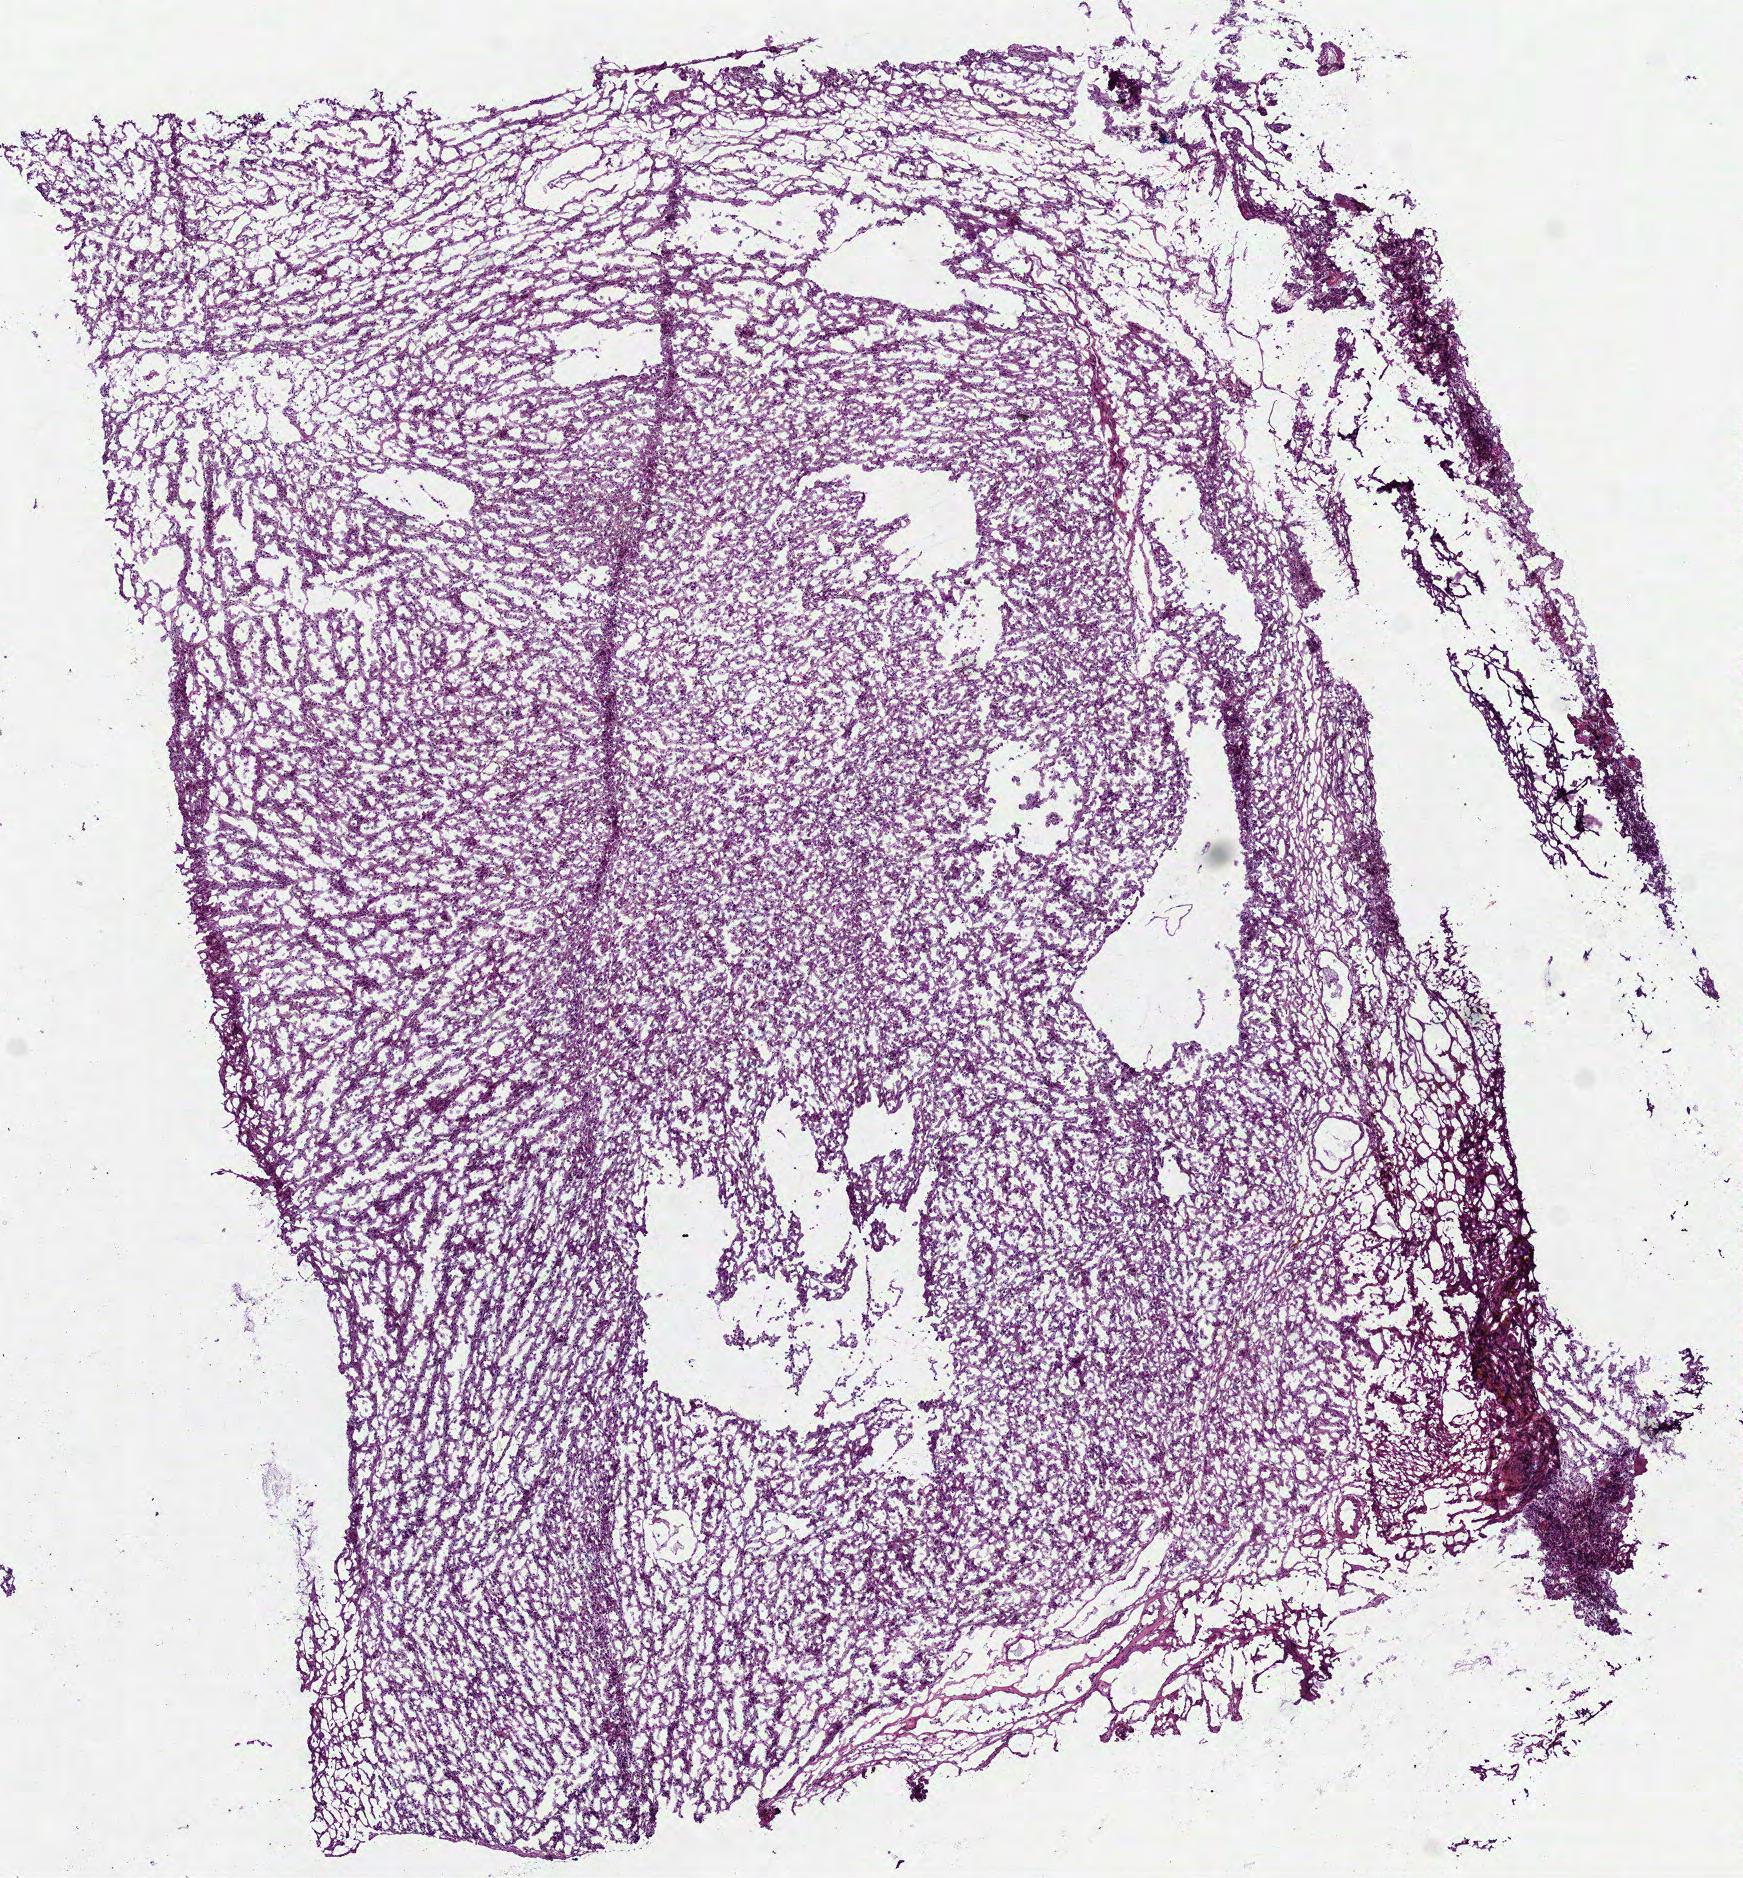
Digitized H&E-stained tissue section (whole slide) — whole scanned area (about 7.0 x 7.6 mm, from a 40x scan) shown as a low-resolution overview, frozen section from the bottom of the tissue portion, brain, primary tumour sample. Female, age 49 years at initial diagnosis. Slide review estimates, as recorded: tumour cells 100%, tumour nuclei 80%, normal cells 0%, stromal cells 0%, necrosis 0%.
Diagnosis: Glioblastoma.